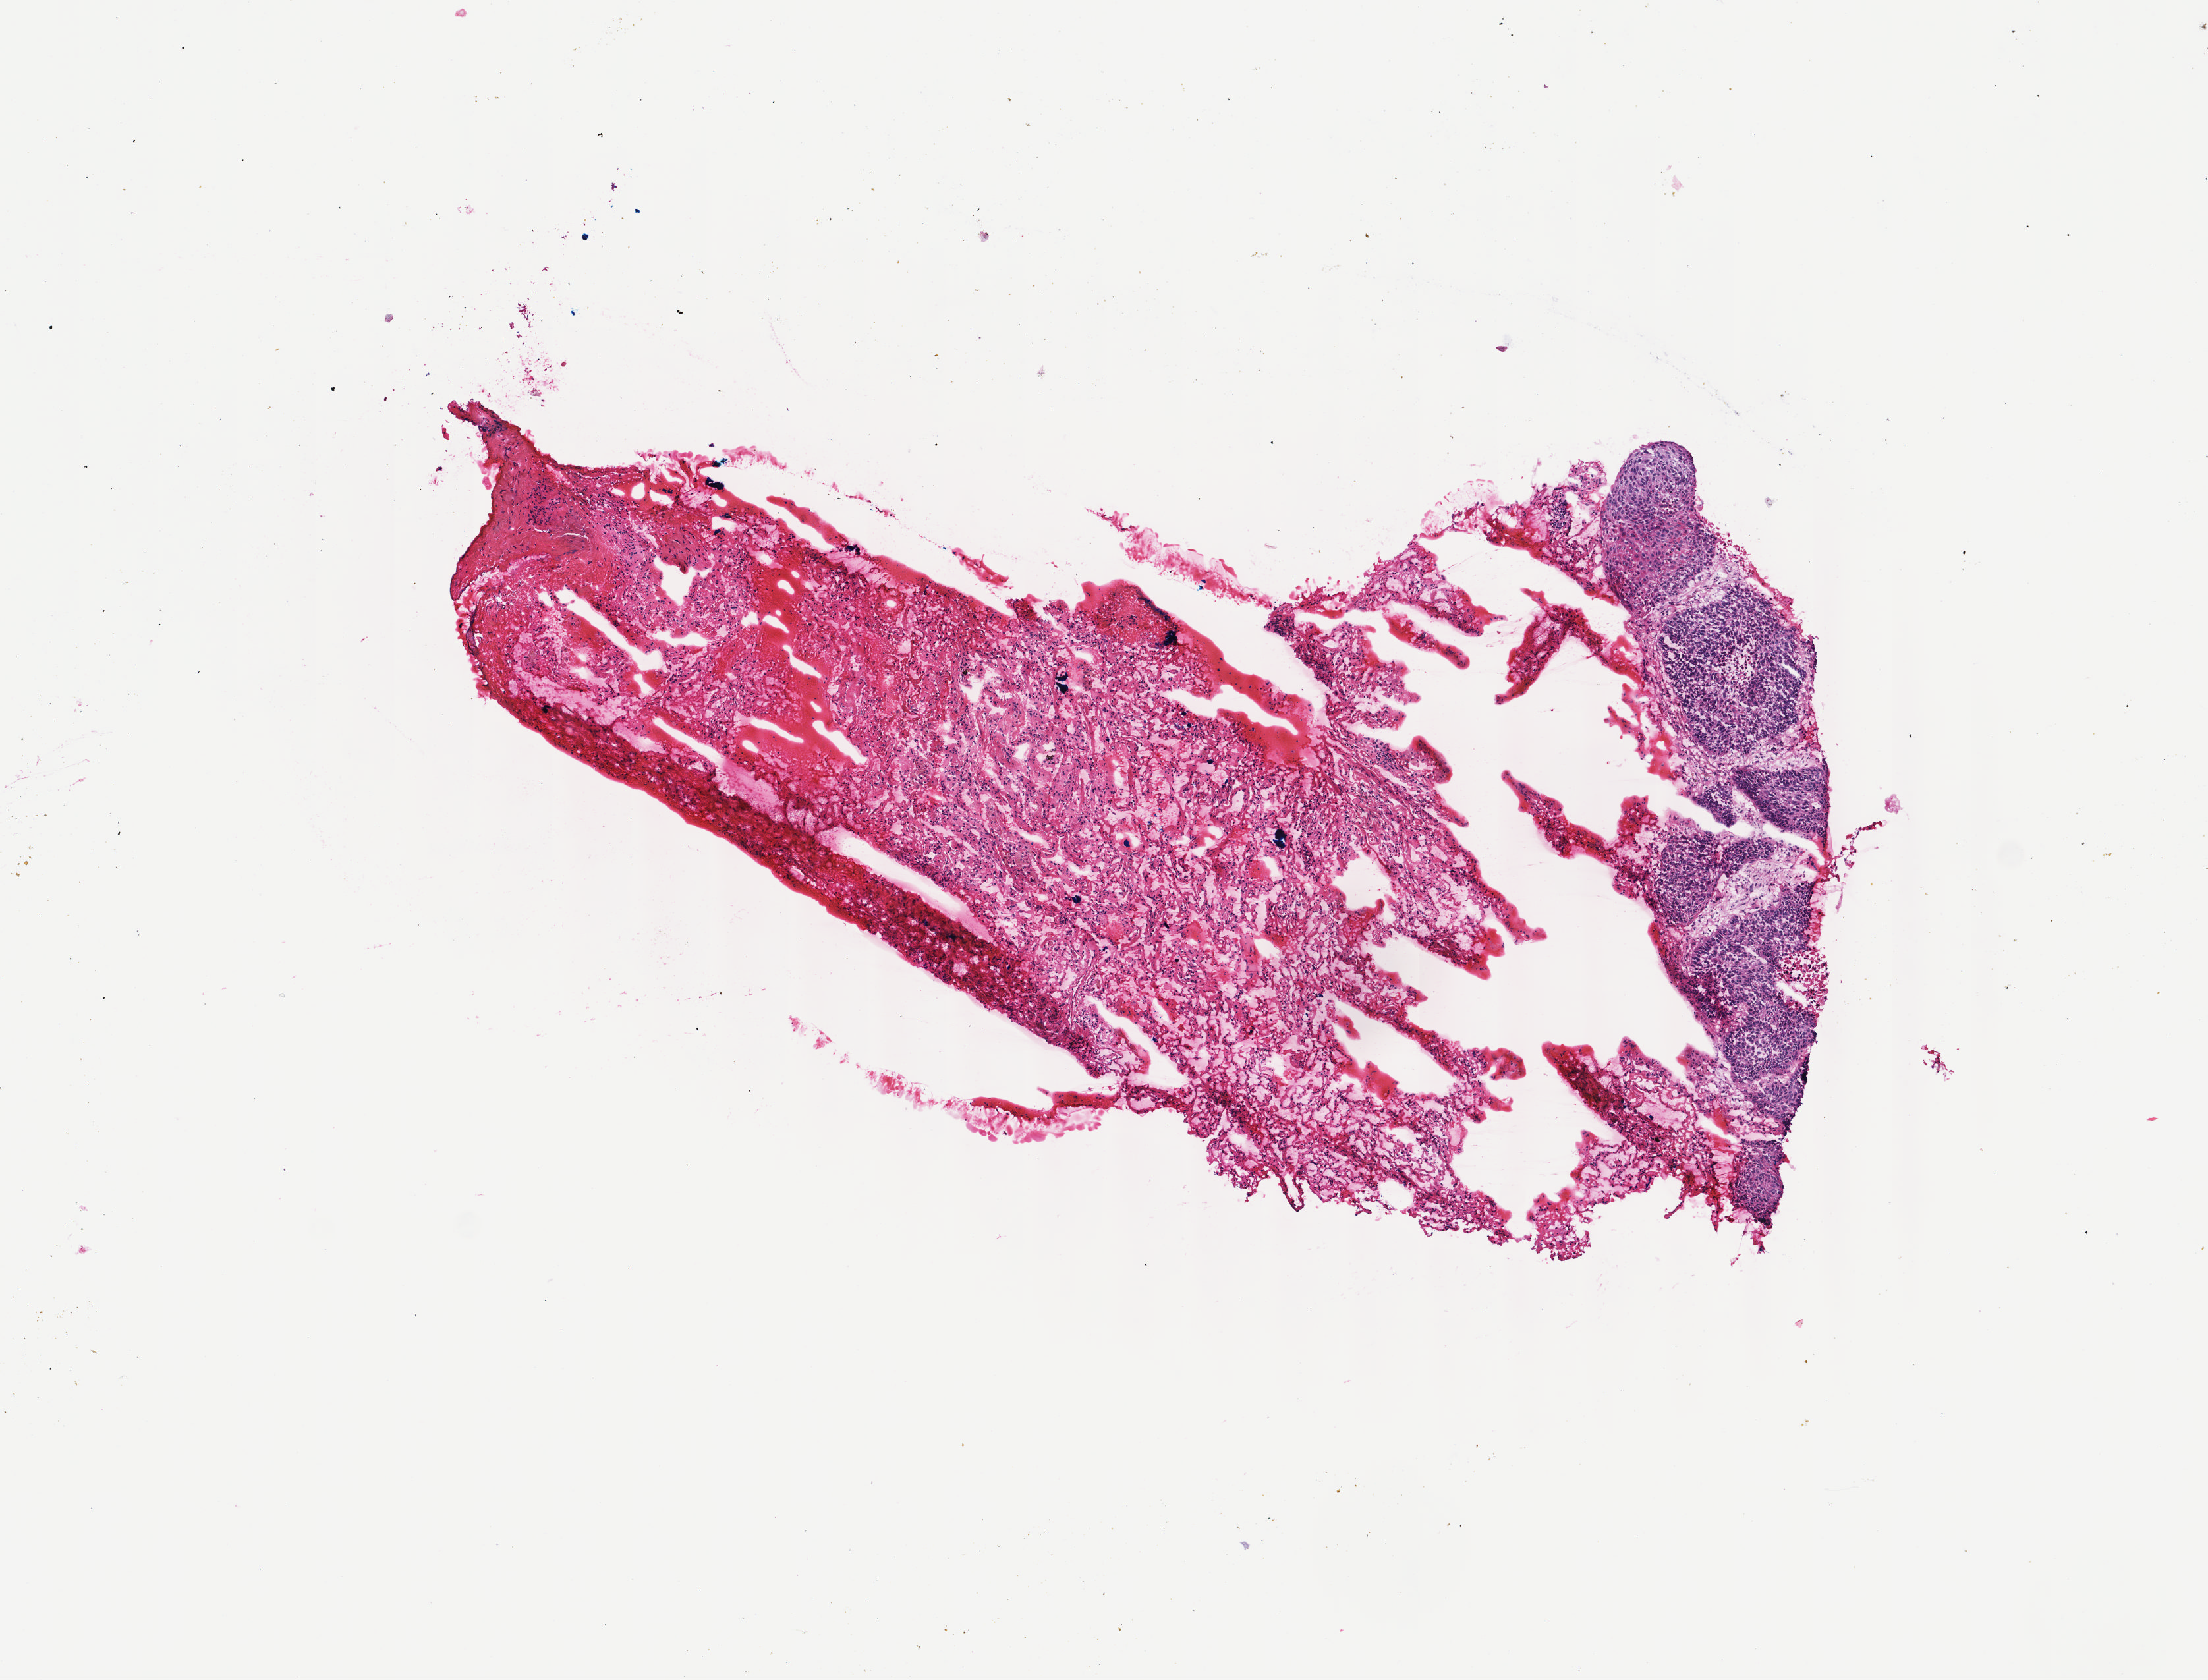
Whole-slide histology image, H&E-stained, whole scanned area (about 6.7 x 5.1 mm, acquisition: 40x scan) shown as a low-resolution overview. Frozen section from the top of the tissue portion. Metastatic tumour sample. Patient: male, age at initial diagnosis 55 years. Slide review estimates, as recorded: tumour cells 22%, tumour nuclei 60%, normal cells 0%, stromal cells 75%, necrosis 3%. Inflammatory infiltration, as recorded: lymphocyte infiltration 6%, monocyte infiltration 3%, neutrophil infiltration 3%.
This section: metastatic tumour tissue. Patient diagnosis: Squamous cell carcinoma, NOS (primary site: middle third of esophagus).